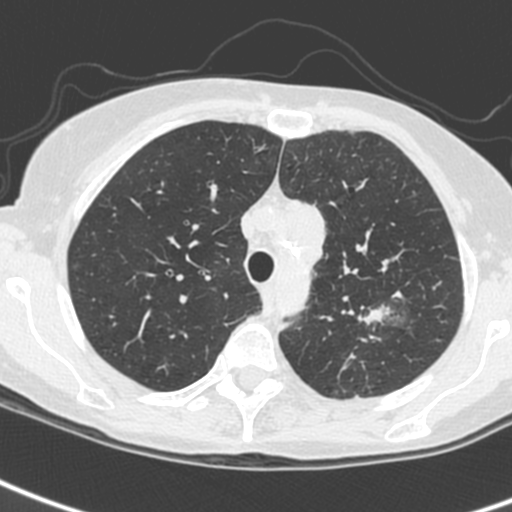
Chest CT (low-dose screening protocol), one axial image. First (baseline) screen. Lung window (W 1500 / L -600 HU). 1.3 mm slice thickness. 512 × 512 image matrix. Female, age 61 years at enrolment. Current smoker at enrolment.
• Lesion marked by an expert reader, bounding box (x1, y1, x2, y2) in pixels: (344, 291, 411, 347).
• The screening reader recorded 2 non-calcified nodules or masses ≥4 mm on this exam (left upper lobe, left upper lobe); which of them this box marks is not recorded.